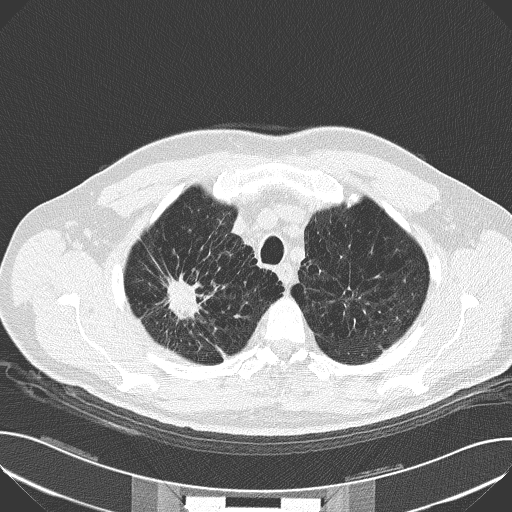
Low-dose screening chest CT, axial slice. Baseline screening round. Lung window (W 1500 / L -600 HU). 2 mm slice thickness. Slice 25 of 159 in the series. 512 × 512 image matrix. Male, age 59 years at enrolment.
Expert-annotated lung lesion, bounding box <154,260,217,328> (left, top, right, bottom; pixels). The screening reader recorded 4 non-calcified nodules or masses ≥4 mm on this exam; which of them this box marks is not recorded. Official screen result: positive, change unspecified: nodule(s) >= 4 mm or enlarging nodule(s), mass(es), or other non-specific abnormalities suspicious for lung cancer. Lung cancer was diagnosed 44 days after this screen: squamous cell carcinoma, NOS, right upper lobe, moderately differentiated (G2), stage IA (AJCC 6th edition), 30 mm at pathology.